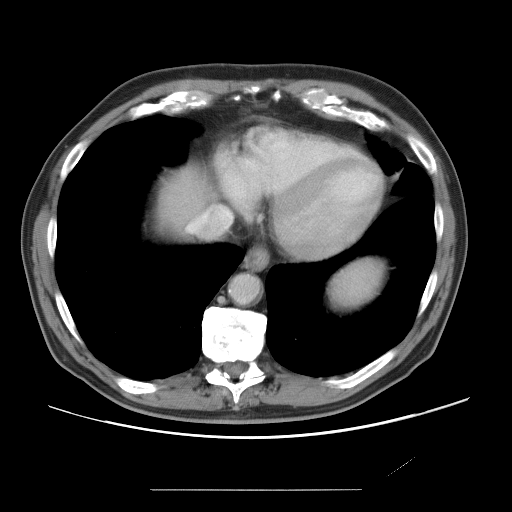
Contrast-enhanced abdominal CT, one axial slice. Soft-tissue window (W 400 / L 40 HU). 512 × 512 image matrix. Male patient, age 74 years. Case-level facts recorded for this patient, not image findings: diagnosis: colorectal cancer liver metastases, imaged before liver resection; multiple liver metastases: yes; largest metastasis: 1.1 cm; disease in both lobes: no.
Outlined on this slice (outlined manually by an expert reader):
- liver: box from (x=150, y=170) to (x=208, y=237) px
- planned liver remnant (the part of the liver to remain after resection): (x=150, y=169)–(x=208, y=234)